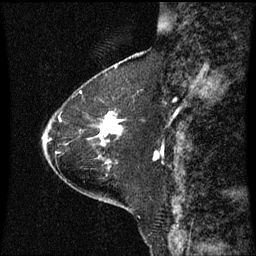
Breast MRI (dynamic contrast-enhanced), one sagittal slice. Slice 22 of 60 in the series (ordered by position). Dynamic contrast-enhanced series, image 2 of 3 at this slice position (ordered by acquisition). 1.5 T. TE 4.2 ms, TR 8.9 ms. 256 × 256 image matrix, field of view 200 × 200 mm. Female patient, age 63 years. Case-level facts recorded for this patient, not image findings: setting: breast cancer imaged before/during neoadjuvant chemotherapy; receptor status: HR-positive, HER2-negative.
Annotated regions visible in this slice (semi-automatically segmented with operator editing):
- analysis volume of interest (the breast-tissue region the enhancement analysis was run in; not a lesion): bounding box [x1, y1, x2, y2] px = [88, 112, 122, 145]
- tumour enhancement mask (voxels above the 70 % enhancement threshold inside the analysis volume of interest): [99, 112, 122, 145]